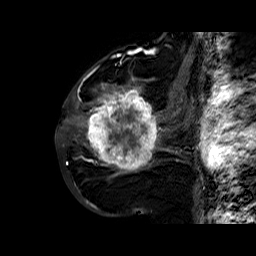
Breast MRI (dynamic contrast-enhanced), one sagittal slice; dynamic contrast-enhanced series, time point 2 of 6 at this slice position (early post-contrast); 1.5 T; TE 6.4 ms, TR 32.8 ms; 4 mm slice thickness; 256 × 256 image matrix, field of view 200 × 200 mm. Female patient. From the clinical record (not read from this slice): setting: breast cancer imaged before/during neoadjuvant chemotherapy; receptor status: HR-positive, HER2-negative.
Annotated regions visible in this slice (semi-automatically segmented with operator editing):
- analysis volume of interest (the breast-tissue region the enhancement analysis was run in; not a lesion): bounding box (x1, y1, x2, y2) in pixels: (86, 77, 163, 177)
- tumour enhancement mask (voxels above the 100 % enhancement threshold inside the analysis volume of interest): (86, 78, 161, 171)